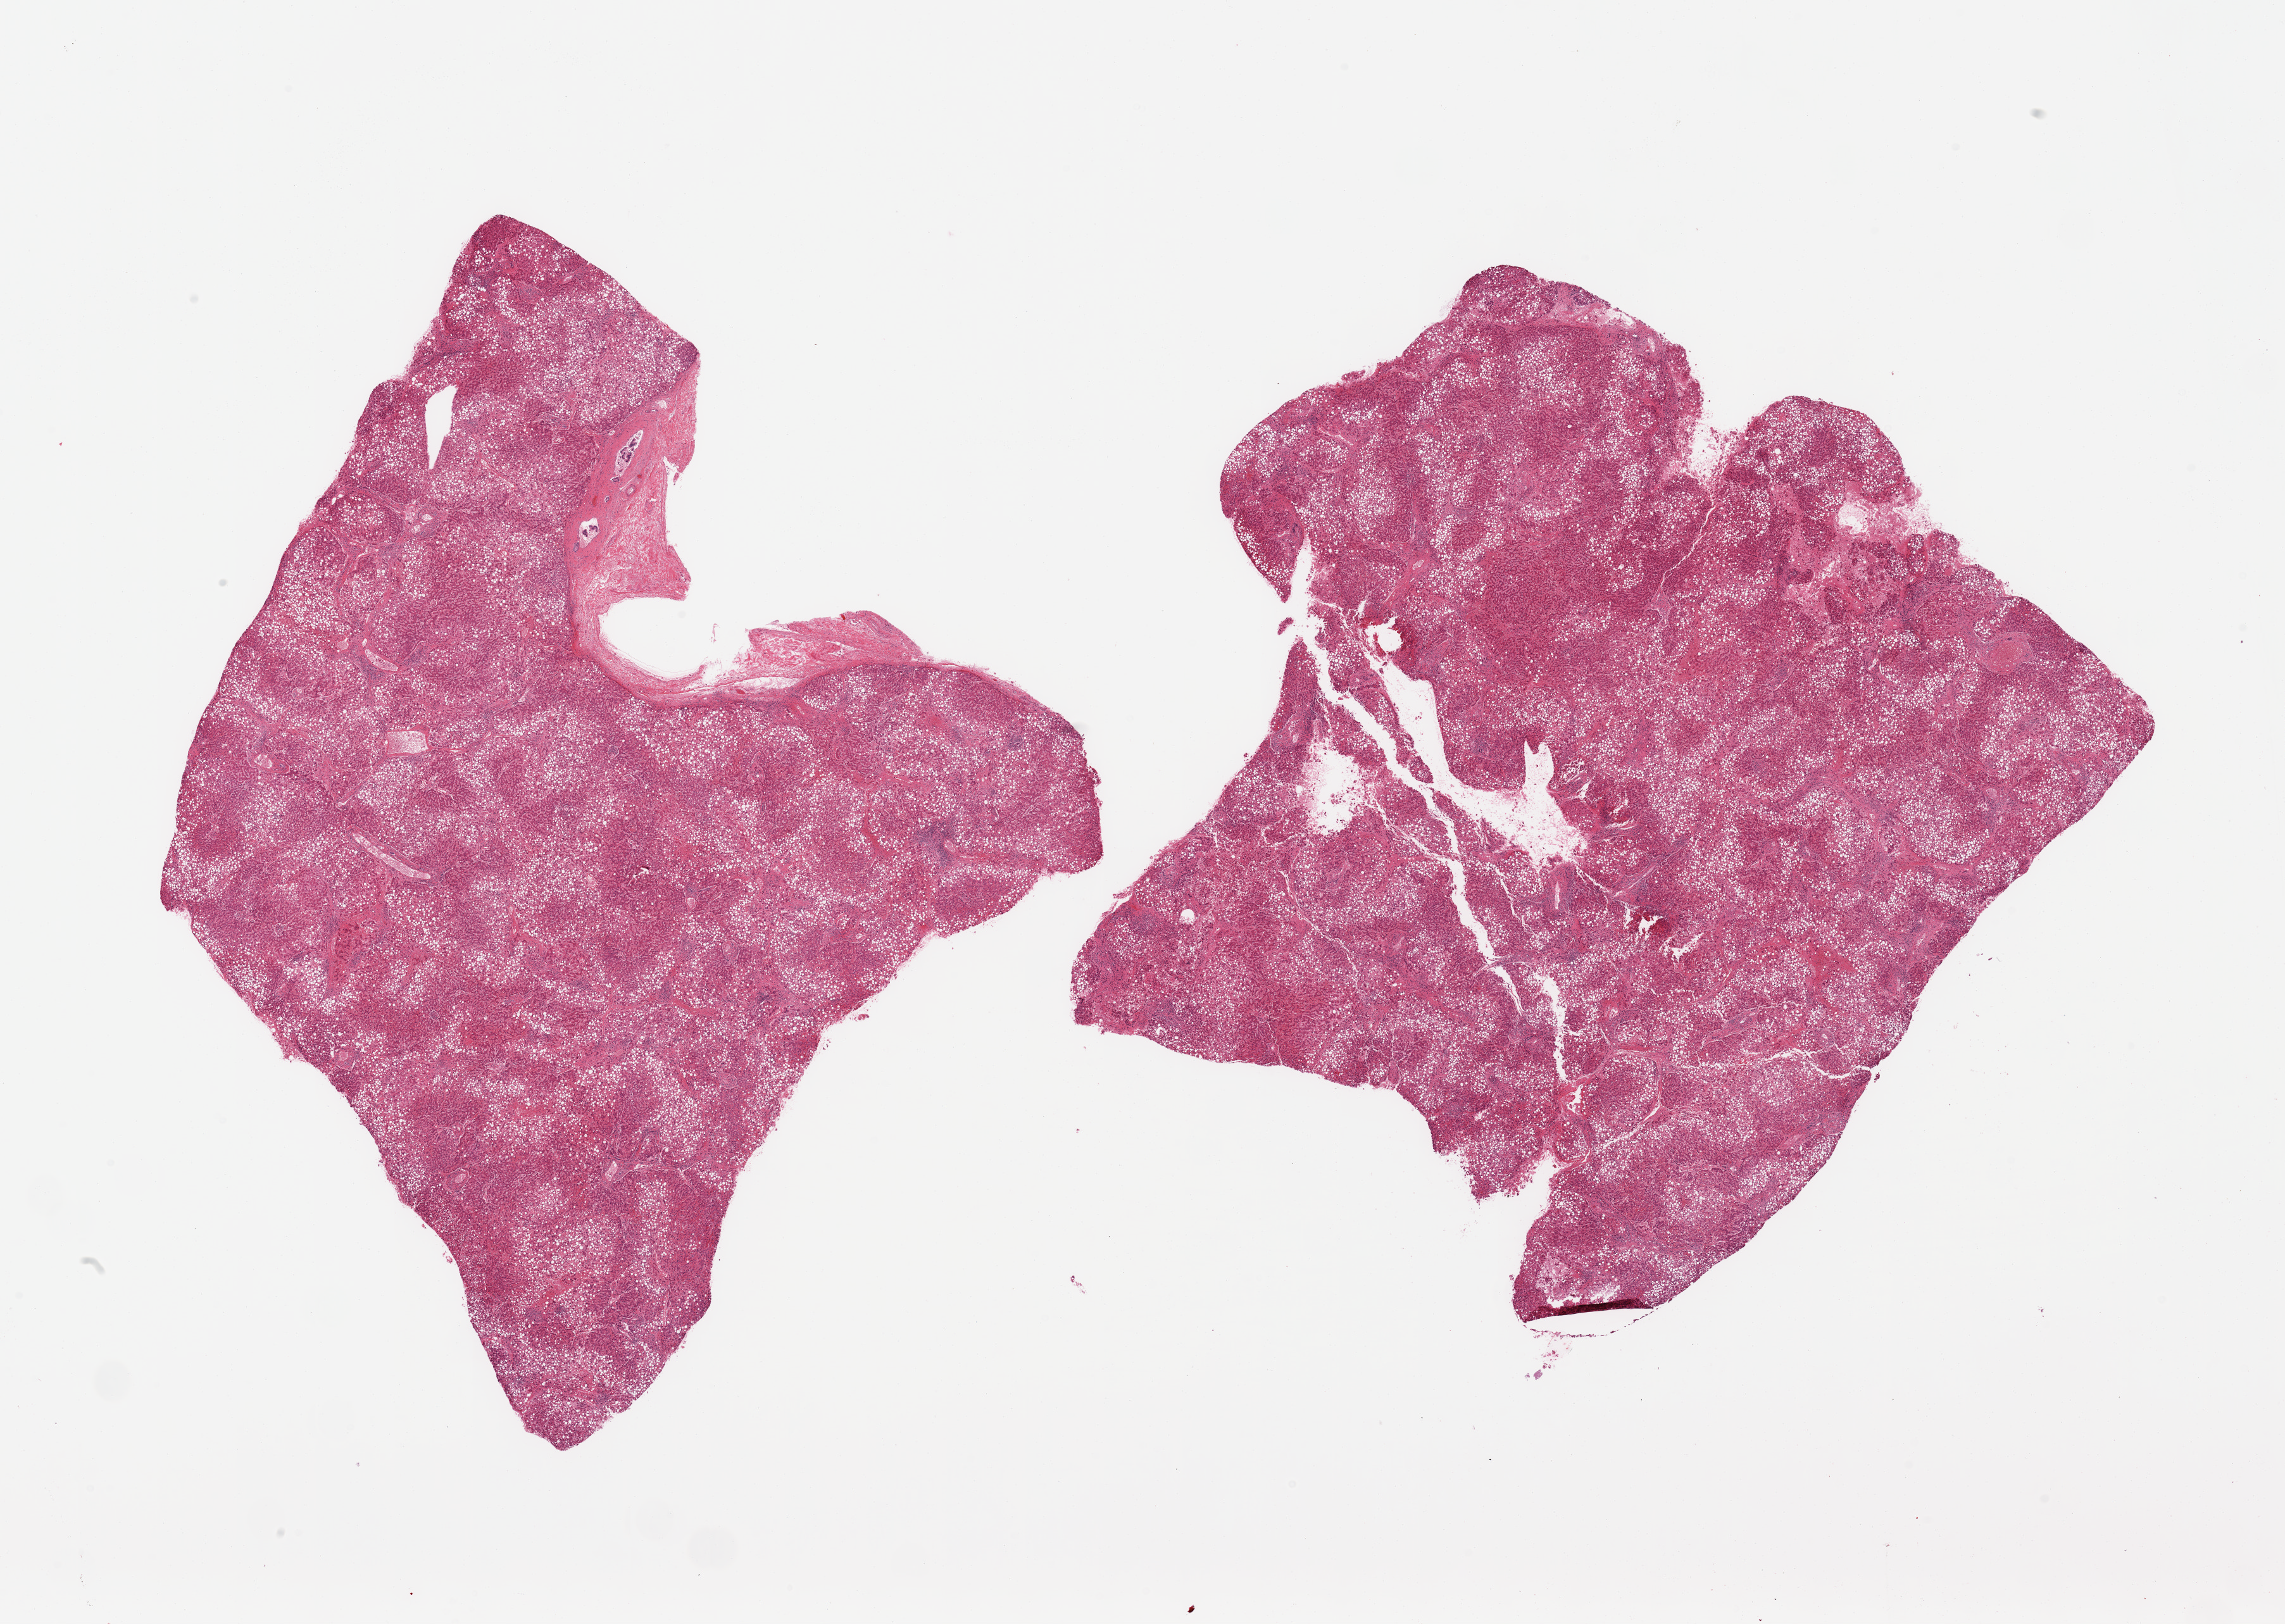
Whole-slide image, hematoxylin and eosin (H&E) stain, brightfield, low-resolution overview of the scanned area, about 28.5 x 20.3 mm, PAXgene-fixed, paraffin-embedded tissue, sampled site (target tissue): liver, donor tissue sample.
Reviewer comment on this tissue sample: 2 pieces; moderate macrovesicular steatosis, cord cell damage, chronic inflammation and bridging fibrosis consistent with steatohepatitis.